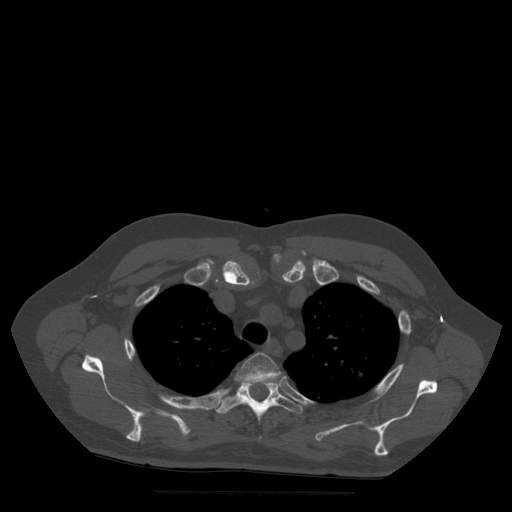
CT including the spine, one axial slice; slice 398 of 522 in the series (ordered by position); bone window (W 1800 / L 400 HU); 1.25 mm slice thickness; 512 × 512 image matrix, field of view 420 × 420 mm. Patient age 72 years. Case-level facts recorded for this patient, not image findings: primary cancer: prostate.
Annotated regions visible in this slice (semi-automatically segmented with operator editing):
- T3 vertebra: bounding box (x1, y1, x2, y2) in pixels: (237, 353, 281, 384)
- T4 vertebra: (215, 380, 303, 423)